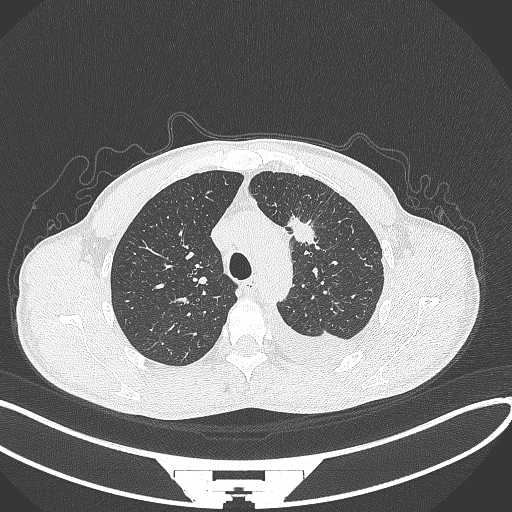
Chest CT, one axial slice; position 250 of 371 along the scan axis; reconstruction kernel B70f; lung window (W 1500 / L -600 HU); 1 mm slice thickness; 512 × 512 image matrix, field of view 400 × 400 mm. Patient: male, 49 years. From the clinical record (not read from this slice): clinical TNM (as recorded): T1c N1 M1.
Annotated regions visible in this slice (bounding box drawn by a radiologist):
- lung tumour (recorded histology: adenocarcinoma): box from (x=290, y=210) to (x=320, y=251) px